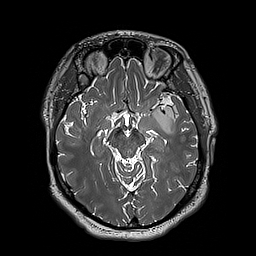
Brain MRI from a brain-tumour surgery series, one axial slice. Slice 116 of 192 in the series (ordered by position). 256 × 256 image matrix, field of view 250 × 250 mm. Case-level facts recorded for this patient, not image findings: histopathology: Astrocytoma; WHO grade: 3; IDH mutation: yes.
Annotated regions visible in this slice (expert manual segmentation):
- tumour: bounding box (x1, y1, x2, y2) in pixels: (152, 104, 178, 134)